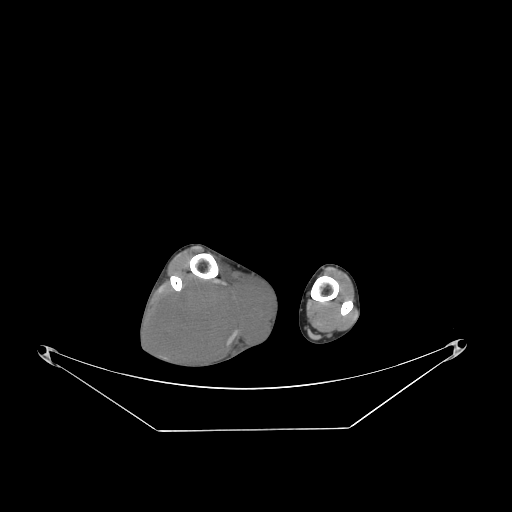
CT of an extremity soft-tissue mass (from a PET/CT study), one axial slice. Slice 65 of 267 in the series (ordered by position). 140 kVp. Soft-tissue window (W 400 / L 40 HU). 512 × 512 image matrix, field of view 500 × 500 mm. Male patient. Case-level facts recorded for this patient, not image findings: histological type: liposarcoma - round cell; grade: high; site of the primary tumour: right calf.
Outlined on this slice (expert contour drawn on MRI and transferred to this co-registered scan by the dataset authors):
- gross tumour volume (mass): bounding box [x1, y1, x2, y2] px = [151, 272, 277, 369]